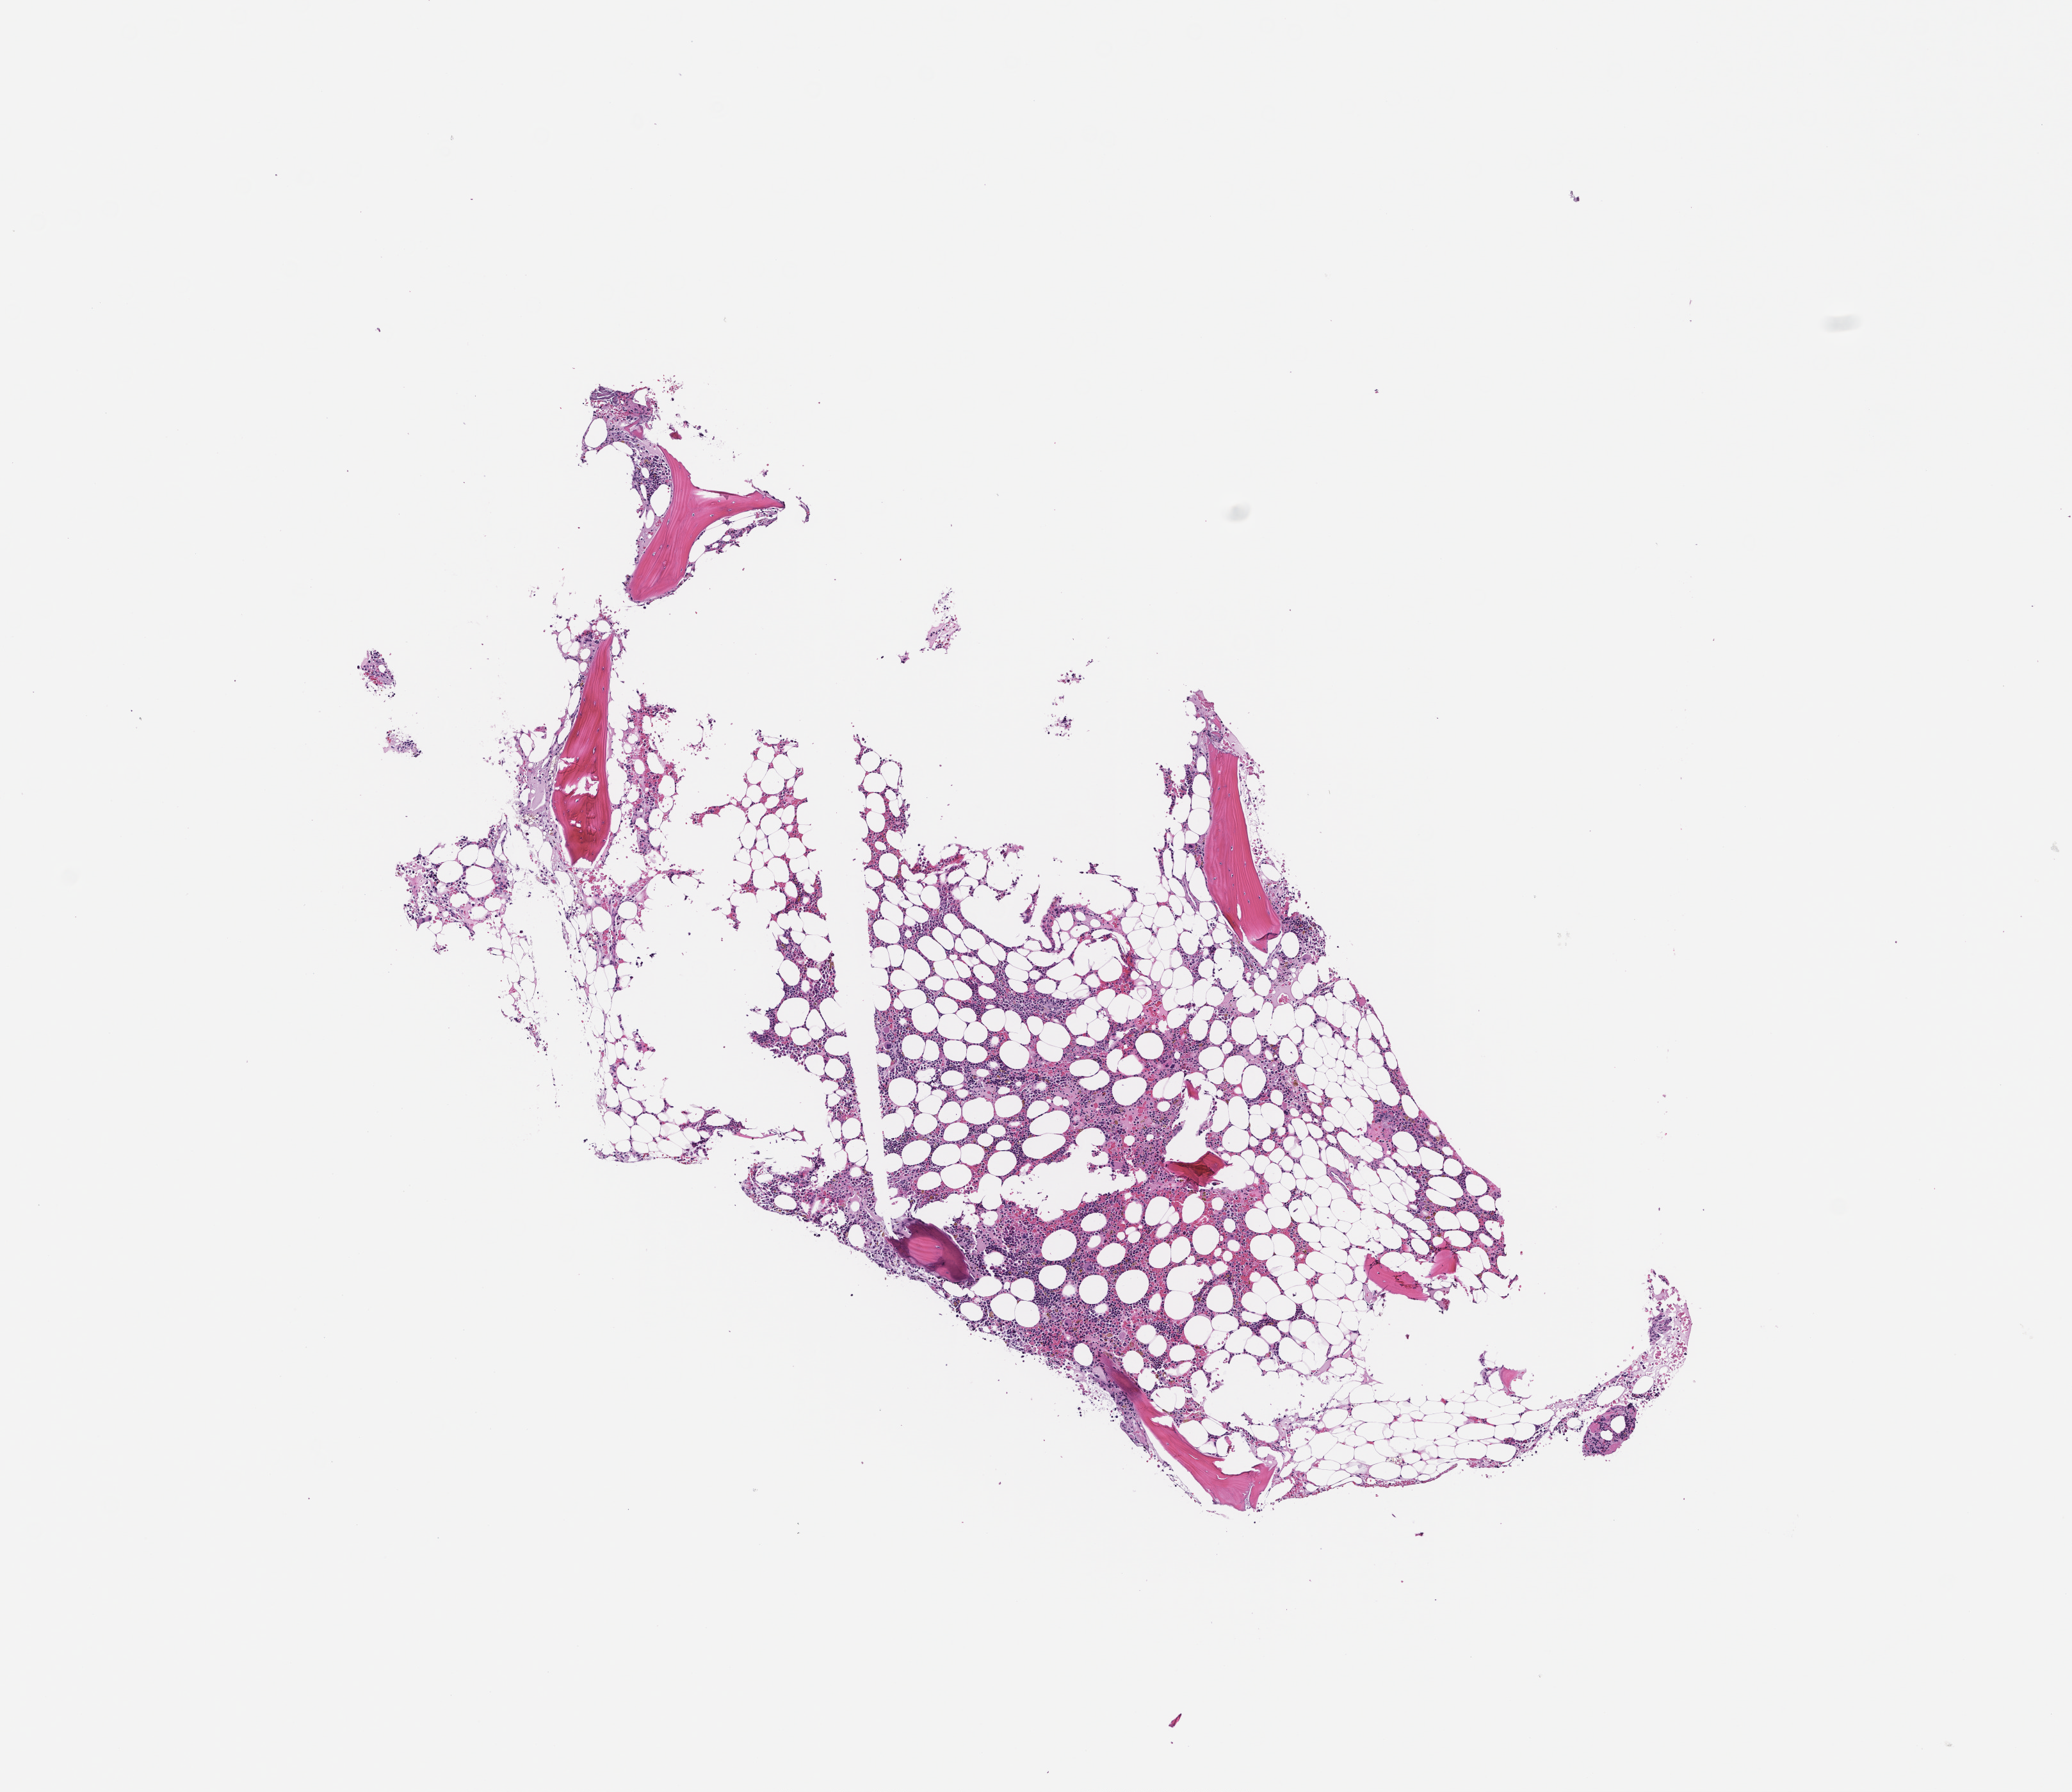
Digitized haematoxylin and eosin-stained section — whole scanned area (about 6.5 x 5.6 mm) shown as a low-resolution overview. Formalin-fixed paraffin-embedded section. Tissue site: bone marrow. Collected at baseline (before treatment). Patient: male.
This section: primary tumor. Diagnosis: Plasma Cell Myeloma.